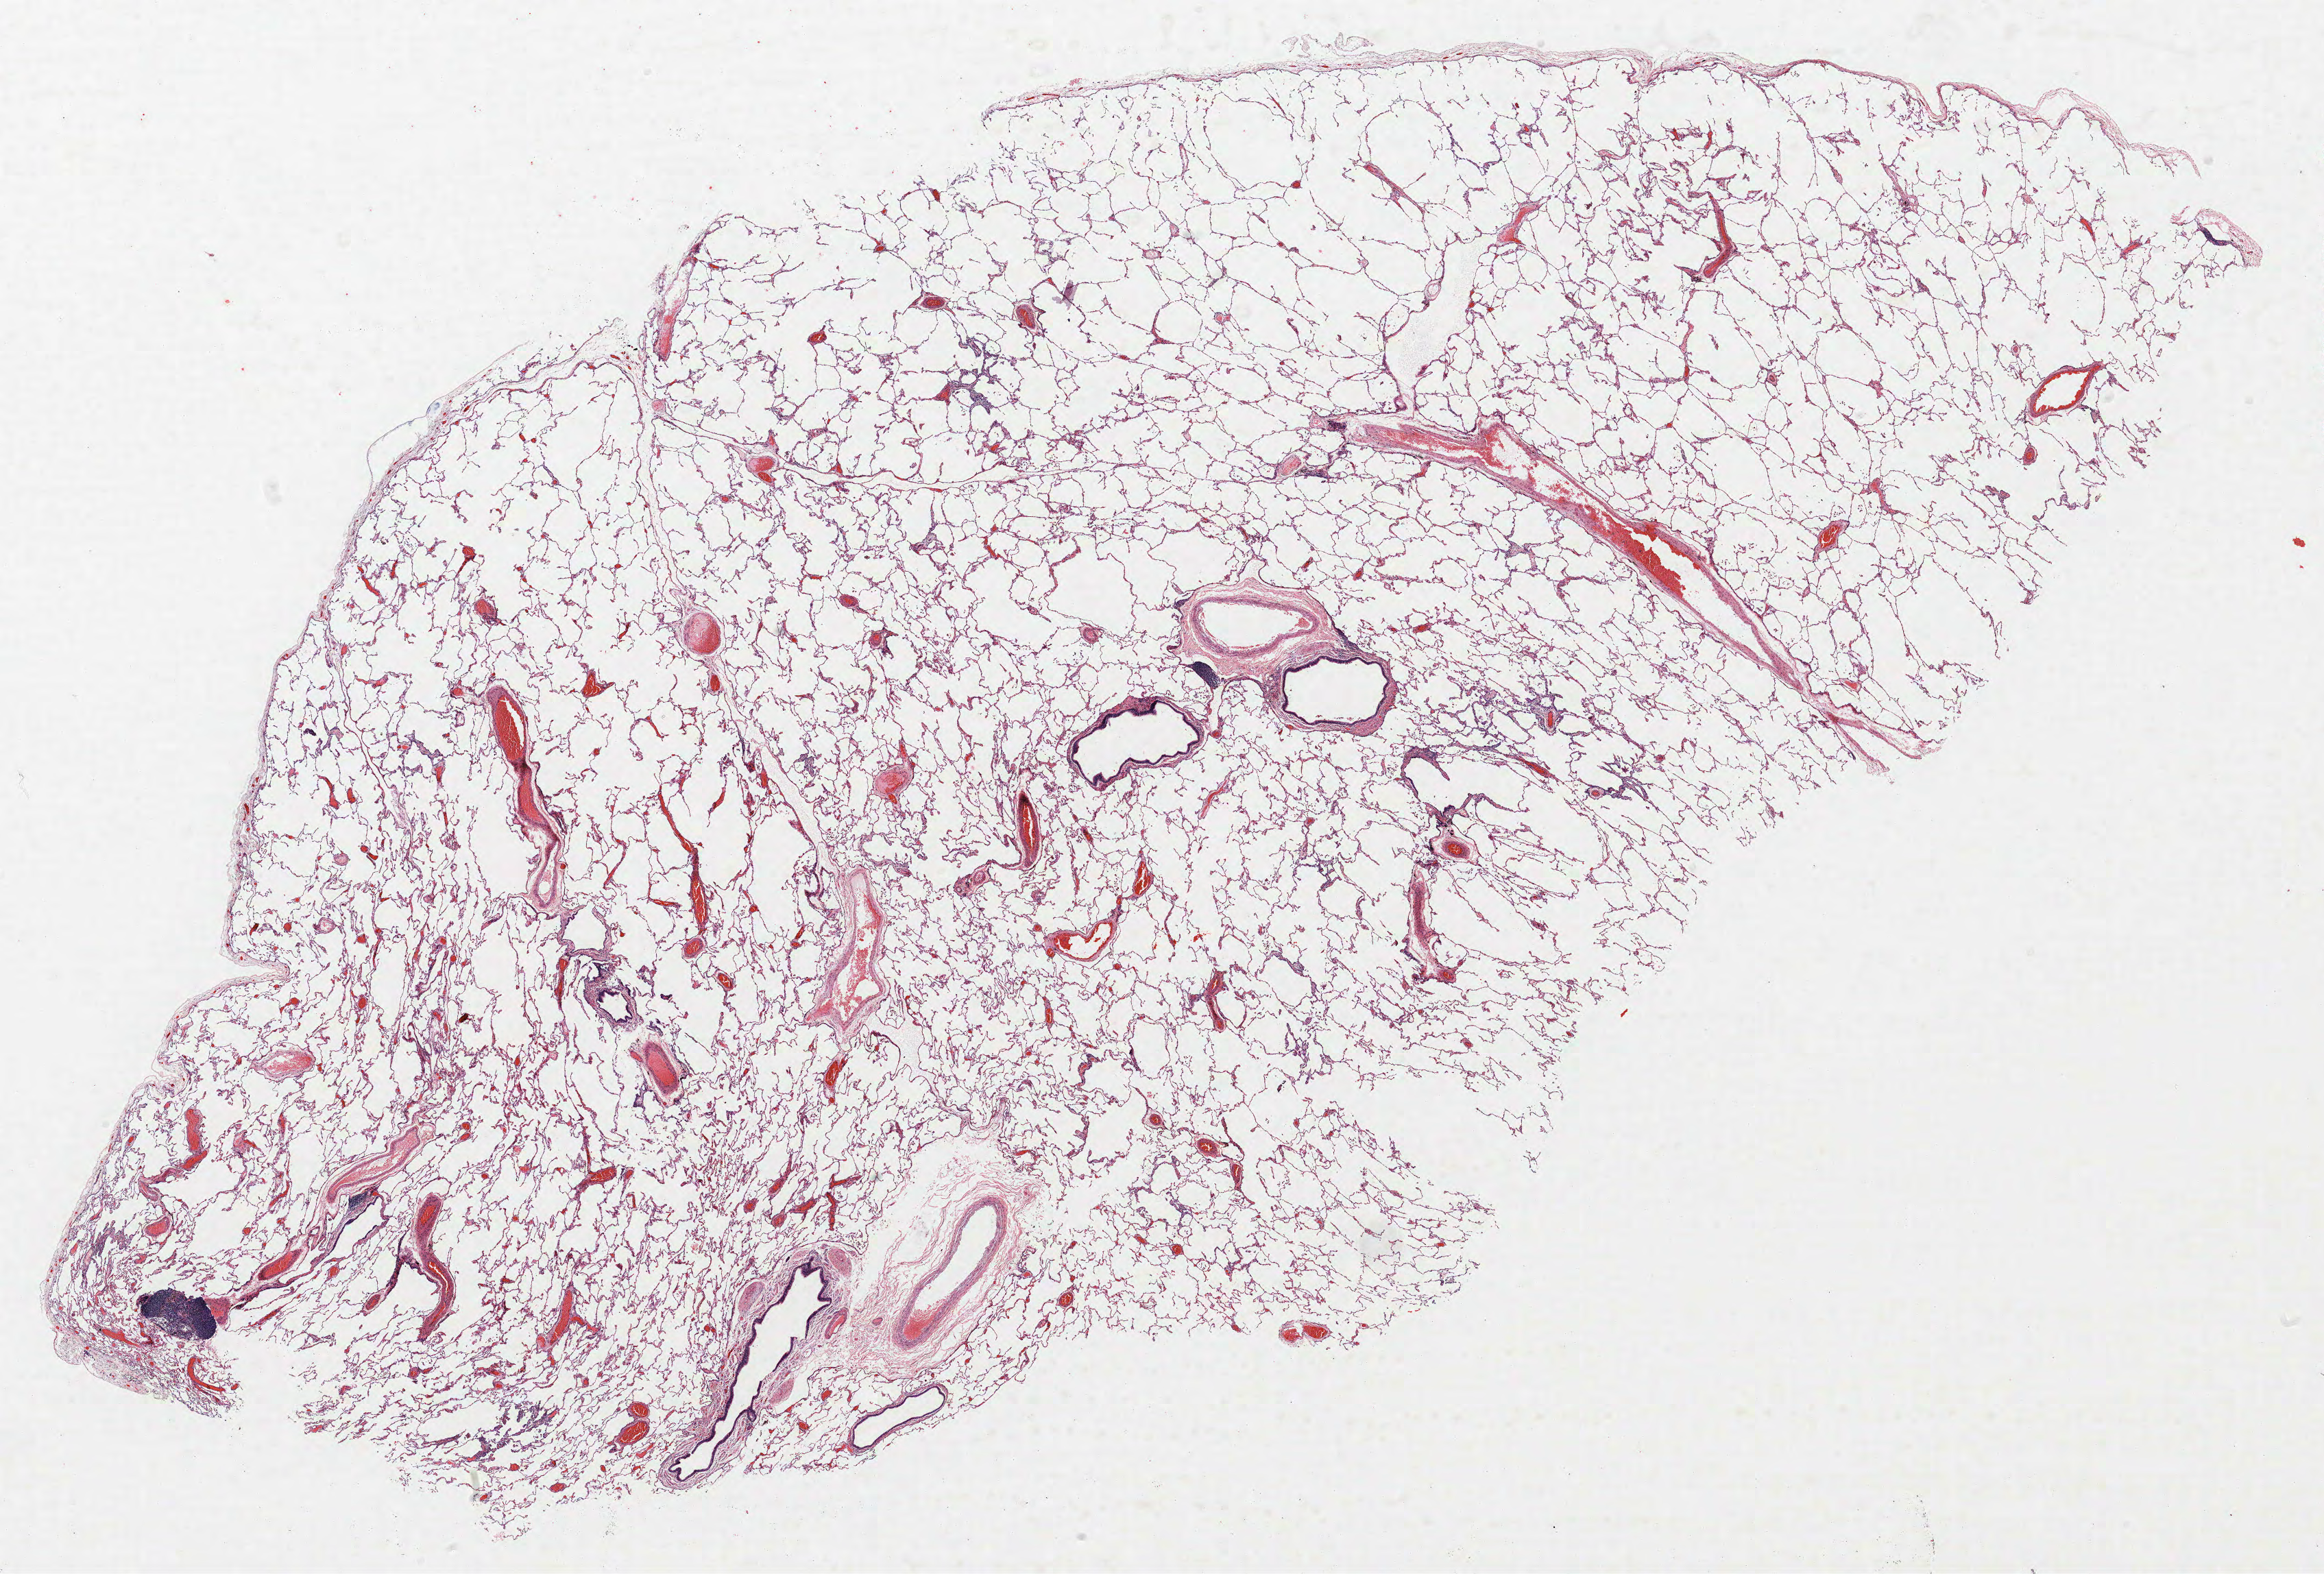
Hematoxylin and eosin (H&E) stained whole-slide image, whole scanned area (about 27.1 x 18.4 mm) shown as a low-resolution overview; FFPE section; lung. Female patient, aged 59 at enrolment. Grade: poorly differentiated (G3).
* stage (AJCC 6th edition): IA
* participant's lung-cancer diagnosis: Large cell neuroendocrine carcinoma
* tumour size (pathology): 12 mm
* primary tumour location (clinical record): left upper lobe